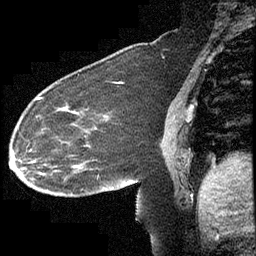
Breast MRI (dynamic contrast-enhanced), one sagittal slice; dynamic contrast-enhanced study with each time point stored as its own series, time point 2 of 4 at this slice position (early post-contrast, ordered by acquisition time); 1.5 T; TE 4.2 ms, TR 6.7 ms; 3 mm slice thickness; 256 × 256 image matrix, field of view 200 × 200 mm. Female patient, age 63 years. Case-level facts recorded for this patient, not image findings: setting: breast cancer imaged before/during neoadjuvant chemotherapy; receptor status: triple-negative.
Annotated regions visible in this slice (semi-automatic segmentation, software-assisted and operator-edited):
- analysis volume of interest (the breast-tissue region the enhancement analysis was run in; not a lesion): bounding box (x1, y1, x2, y2) in pixels: (13, 90, 140, 211)
- tumour enhancement mask (voxels above the 70 % enhancement threshold inside the analysis volume of interest): (38, 97, 78, 167)